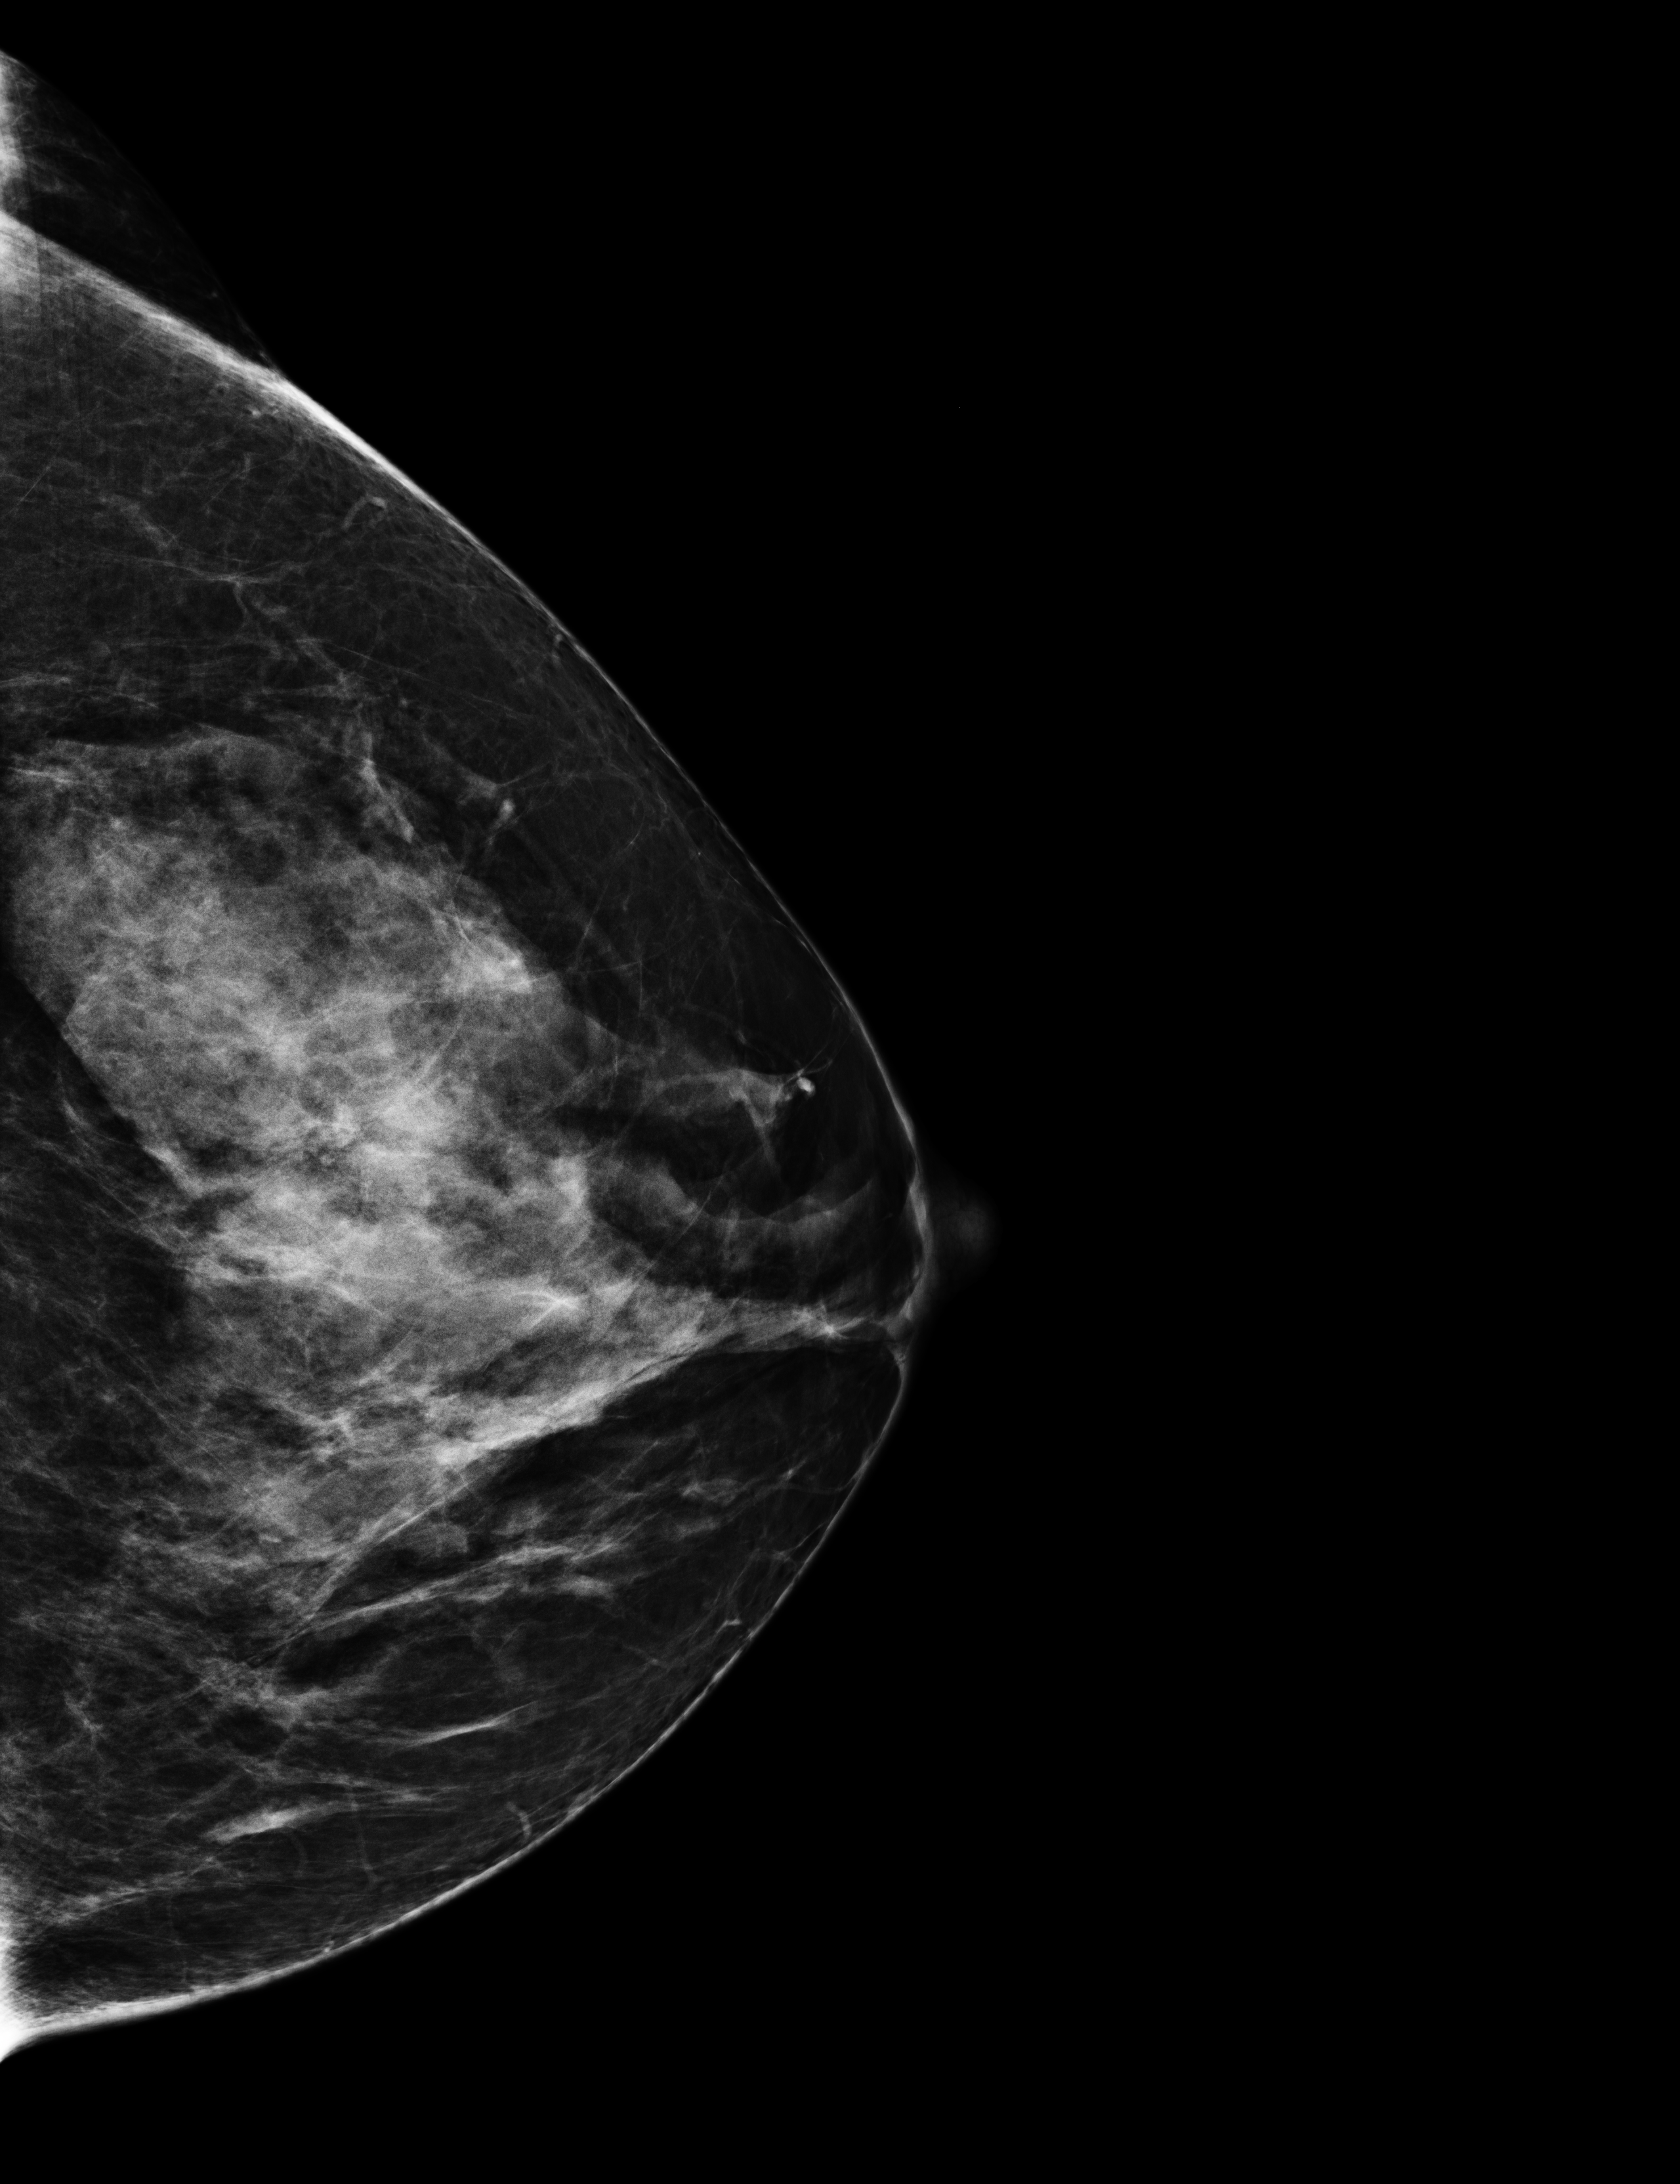
Screening examination. Patient aged 51 years (female).
Image type: full-field digital mammogram. Breast: left. Projection: CC view.